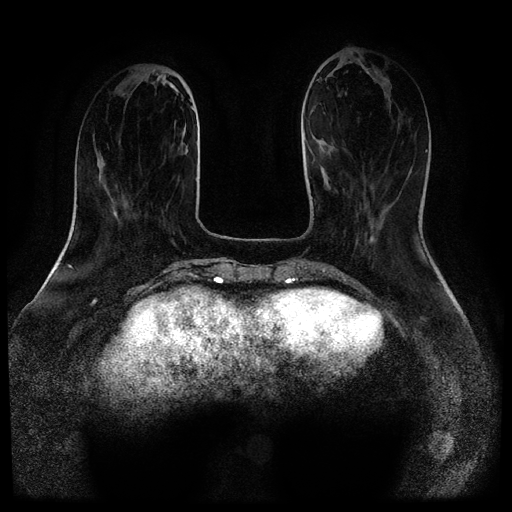
Breast MRI (dynamic contrast-enhanced, multi-phase), one axial slice. Position 33 of 116 along the scan axis. Dynamic contrast-enhanced series, time point 2 of 5 at this slice position (early post-contrast). 1.5 T. TE 2.6 ms, TR 5.3 ms. 512 × 512 image matrix, field of view 360 × 360 mm. Female patient, age 52 years.
Outlined on this slice (semi-automatically segmented with operator editing):
- breast lesion (labelled 'tumour' in the annotation; benign lesions carry a separate 'benign' label): bounding box (x1, y1, x2, y2) in pixels: (370, 236, 375, 243)